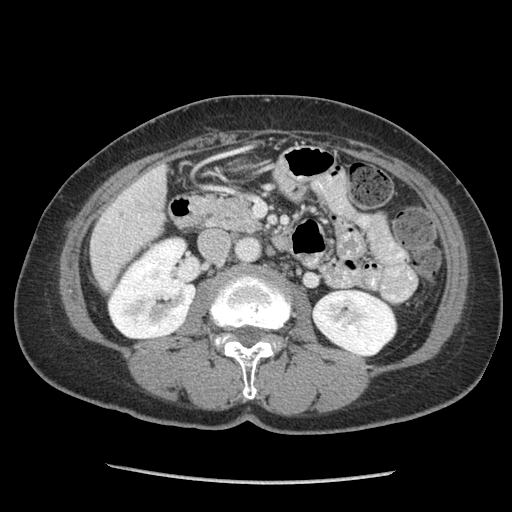
Contrast-enhanced abdominal CT (liver protocol), one axial slice. Position 24 of 105 along the scan axis. Reconstruction kernel STANDARD. 140 kVp. Soft-tissue window (W 400 / L 40 HU). 2.5 mm slice thickness. 512 × 512 image matrix, field of view 340 × 340 mm. Case-level facts recorded for this patient, not image findings: diagnosis: hepatocellular carcinoma (patient treated with transarterial chemoembolisation; whether this scan precedes or follows treatment is not stated here); TNM stage (as recorded): Stage-I; Child-Pugh class: A; tumour differentiation: moderately differentiated; tumour nodularity: uninodular.
Outlined on this slice (semi-automatically segmented with operator editing):
- liver parenchyma outside the tumour (the mass and vessels are separate outlines, so this box may not span the whole liver): bounding box <90,164,166,290> (left, top, right, bottom; pixels)
- liver vessels: <108,171,156,223>